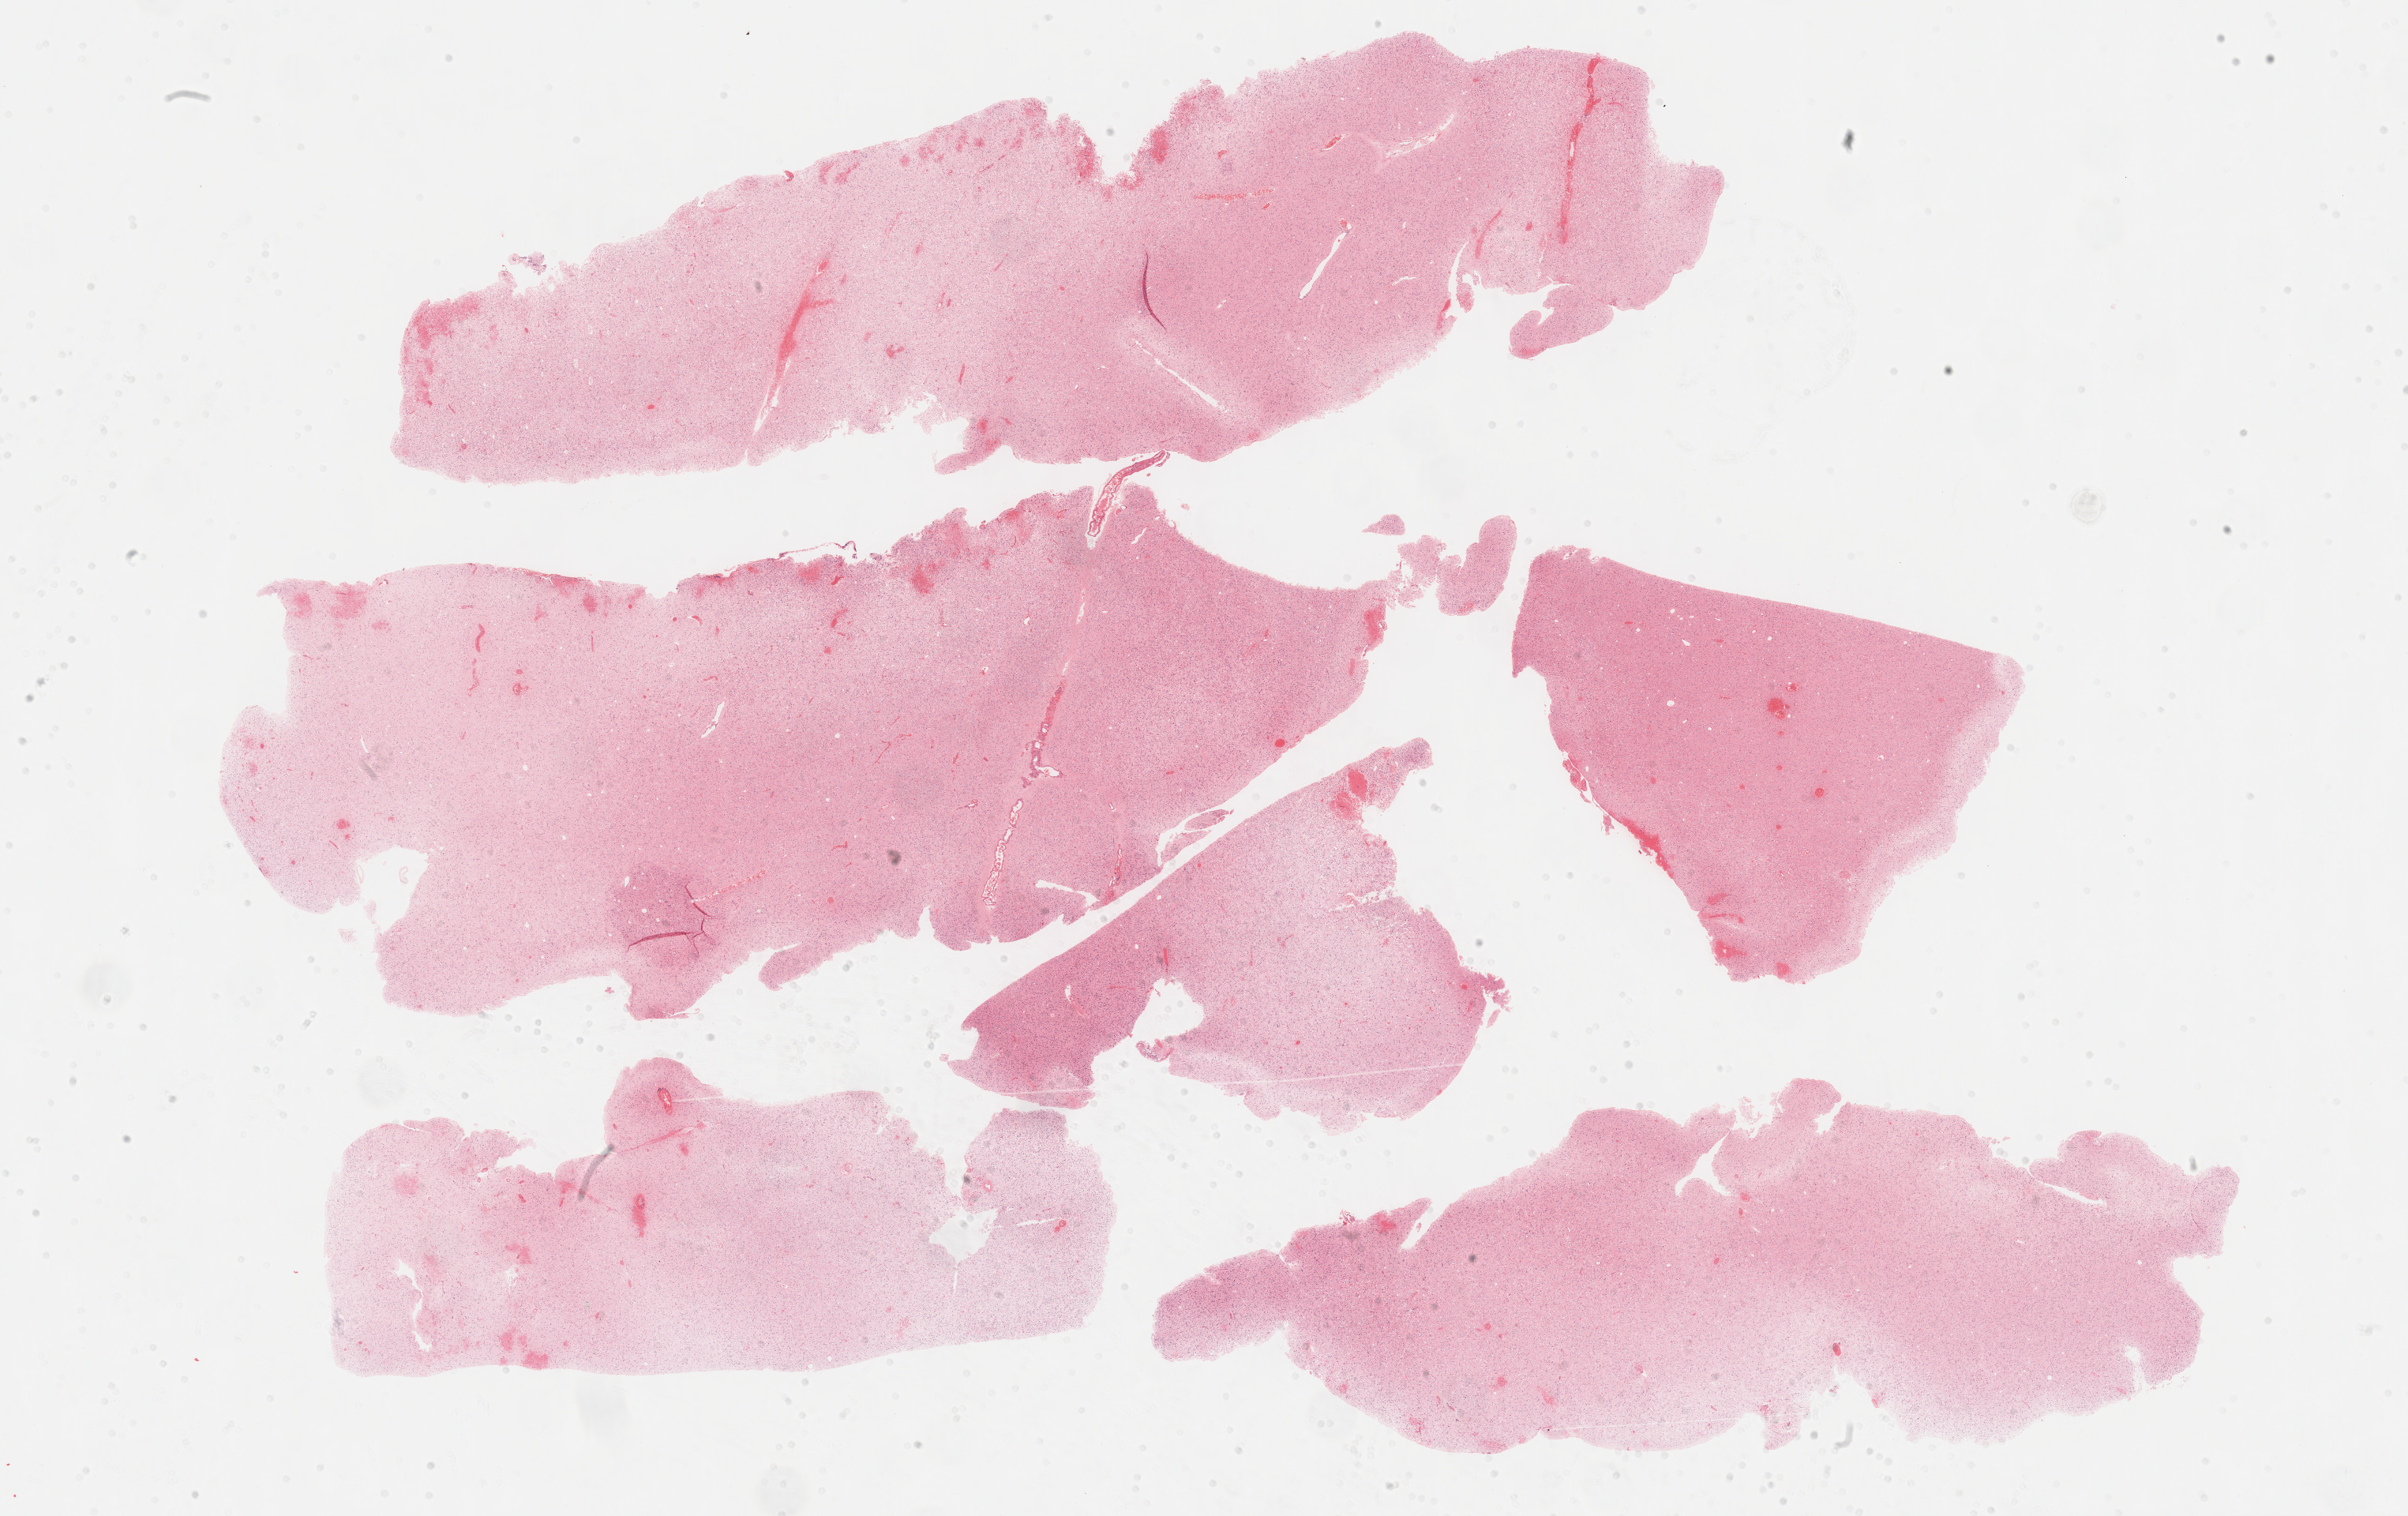
Whole-slide histology image, Hematoxylin and eosin (H&E) stained, a low-resolution overview of the entire scanned area, about 24.7 x 15.5 mm (acquisition: 40x scan). FFPE section. Brain, primary tumour sample. Patient: male, age at initial diagnosis 34 years.
Histologic diagnosis: Oligodendroglioma, NOS (cerebrum).